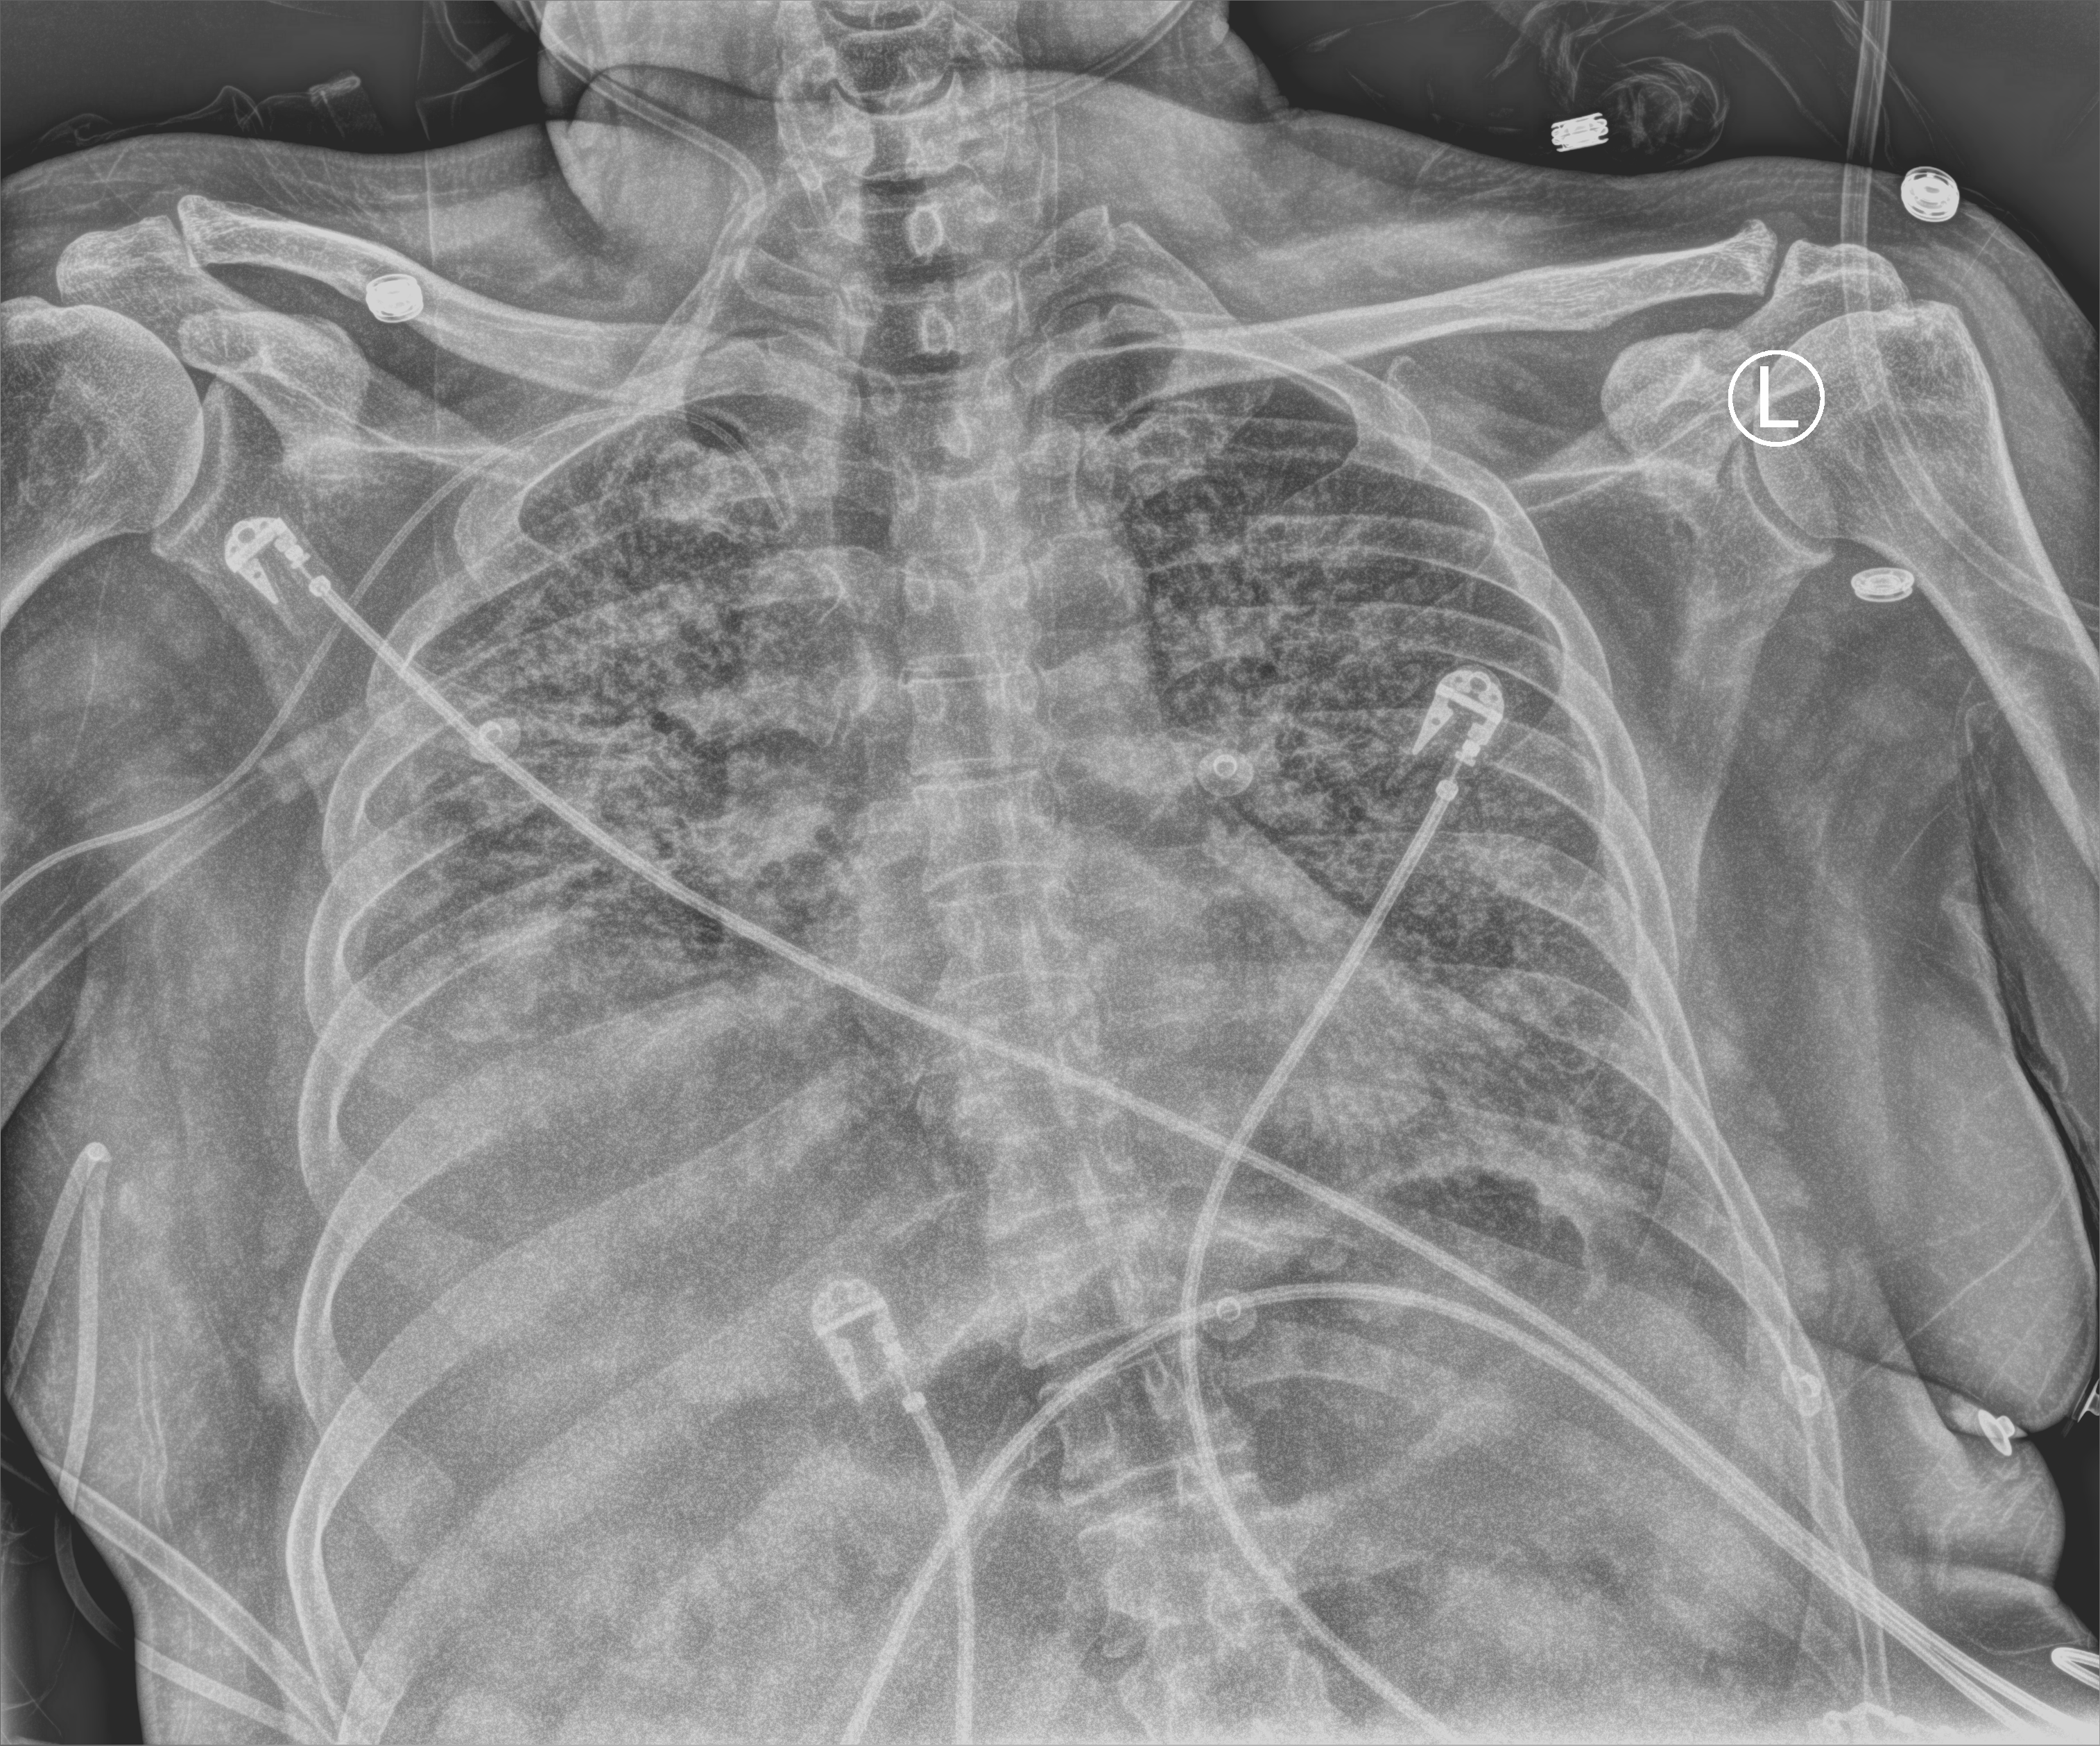
Bedside chest radiograph (computed radiography); anteroposterior (AP) projection. Male patient hospitalised with COVID-19, age 18–59 years.
Hospital-stay facts (about this admission, not read from this image; timing relative to this image not recorded): length of hospital stay: 35 days; mechanically ventilated during this hospital stay: yes.